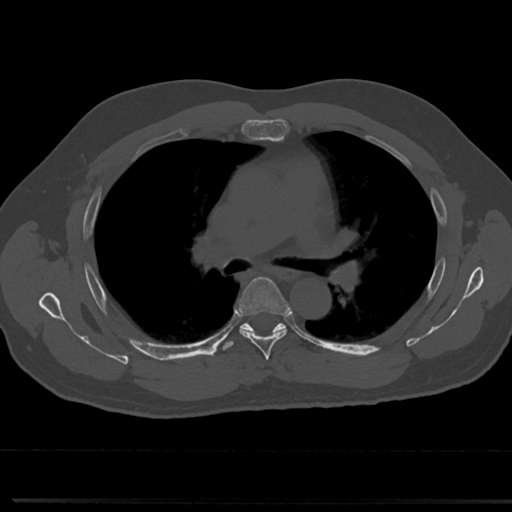
CT including the spine, one axial slice. Position 485 of 817 along the scan axis. Reconstruction kernel Br40s/3. Bone window (W 1800 / L 400 HU). 0.5 mm slice thickness. 512 × 512 image matrix, field of view 355 × 355 mm. Male patient, age 61 years. Case-level facts recorded for this patient, not image findings: primary cancer: prostate.
Annotated regions visible in this slice (semi-automatic segmentation, software-assisted and operator-edited):
- T4 vertebra: bounding box <265,366,273,374> (left, top, right, bottom; pixels)
- T5 vertebra: <235,278,290,353>
- T6 vertebra: <242,327,284,332>